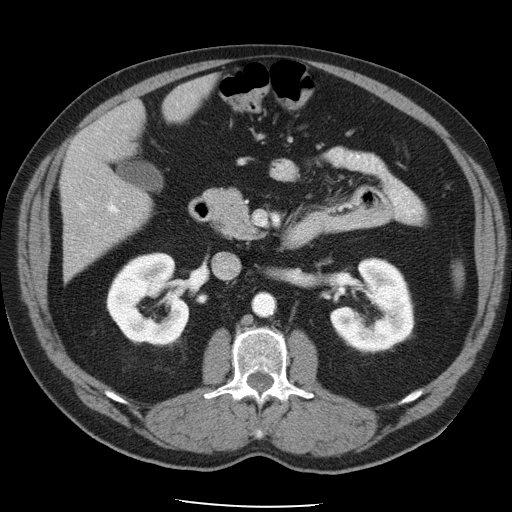
Contrast-enhanced abdominal CT, one axial slice; position 22 of 49 along the scan axis; reconstruction kernel STANDARD; 120 kVp; intravenous contrast given; soft-tissue window (W 400 / L 40 HU); 5 mm slice thickness; 512 × 512 image matrix, field of view 395 × 395 mm. Male patient, age 68 years. From the clinical record (not read from this slice): diagnosis: colorectal cancer liver metastases, imaged before liver resection; multiple liver metastases: yes; largest metastasis: 1.7 cm; disease in both lobes: no.
Annotated regions visible in this slice (outlined manually by an expert reader):
- hepatic veins: bounding box <80,205,84,208> (left, top, right, bottom; pixels)
- liver: <62,79,212,276>
- planned liver remnant (the part of the liver to remain after resection): <64,79,213,236>
- portal vein (with intrahepatic branches): <108,126,131,222>